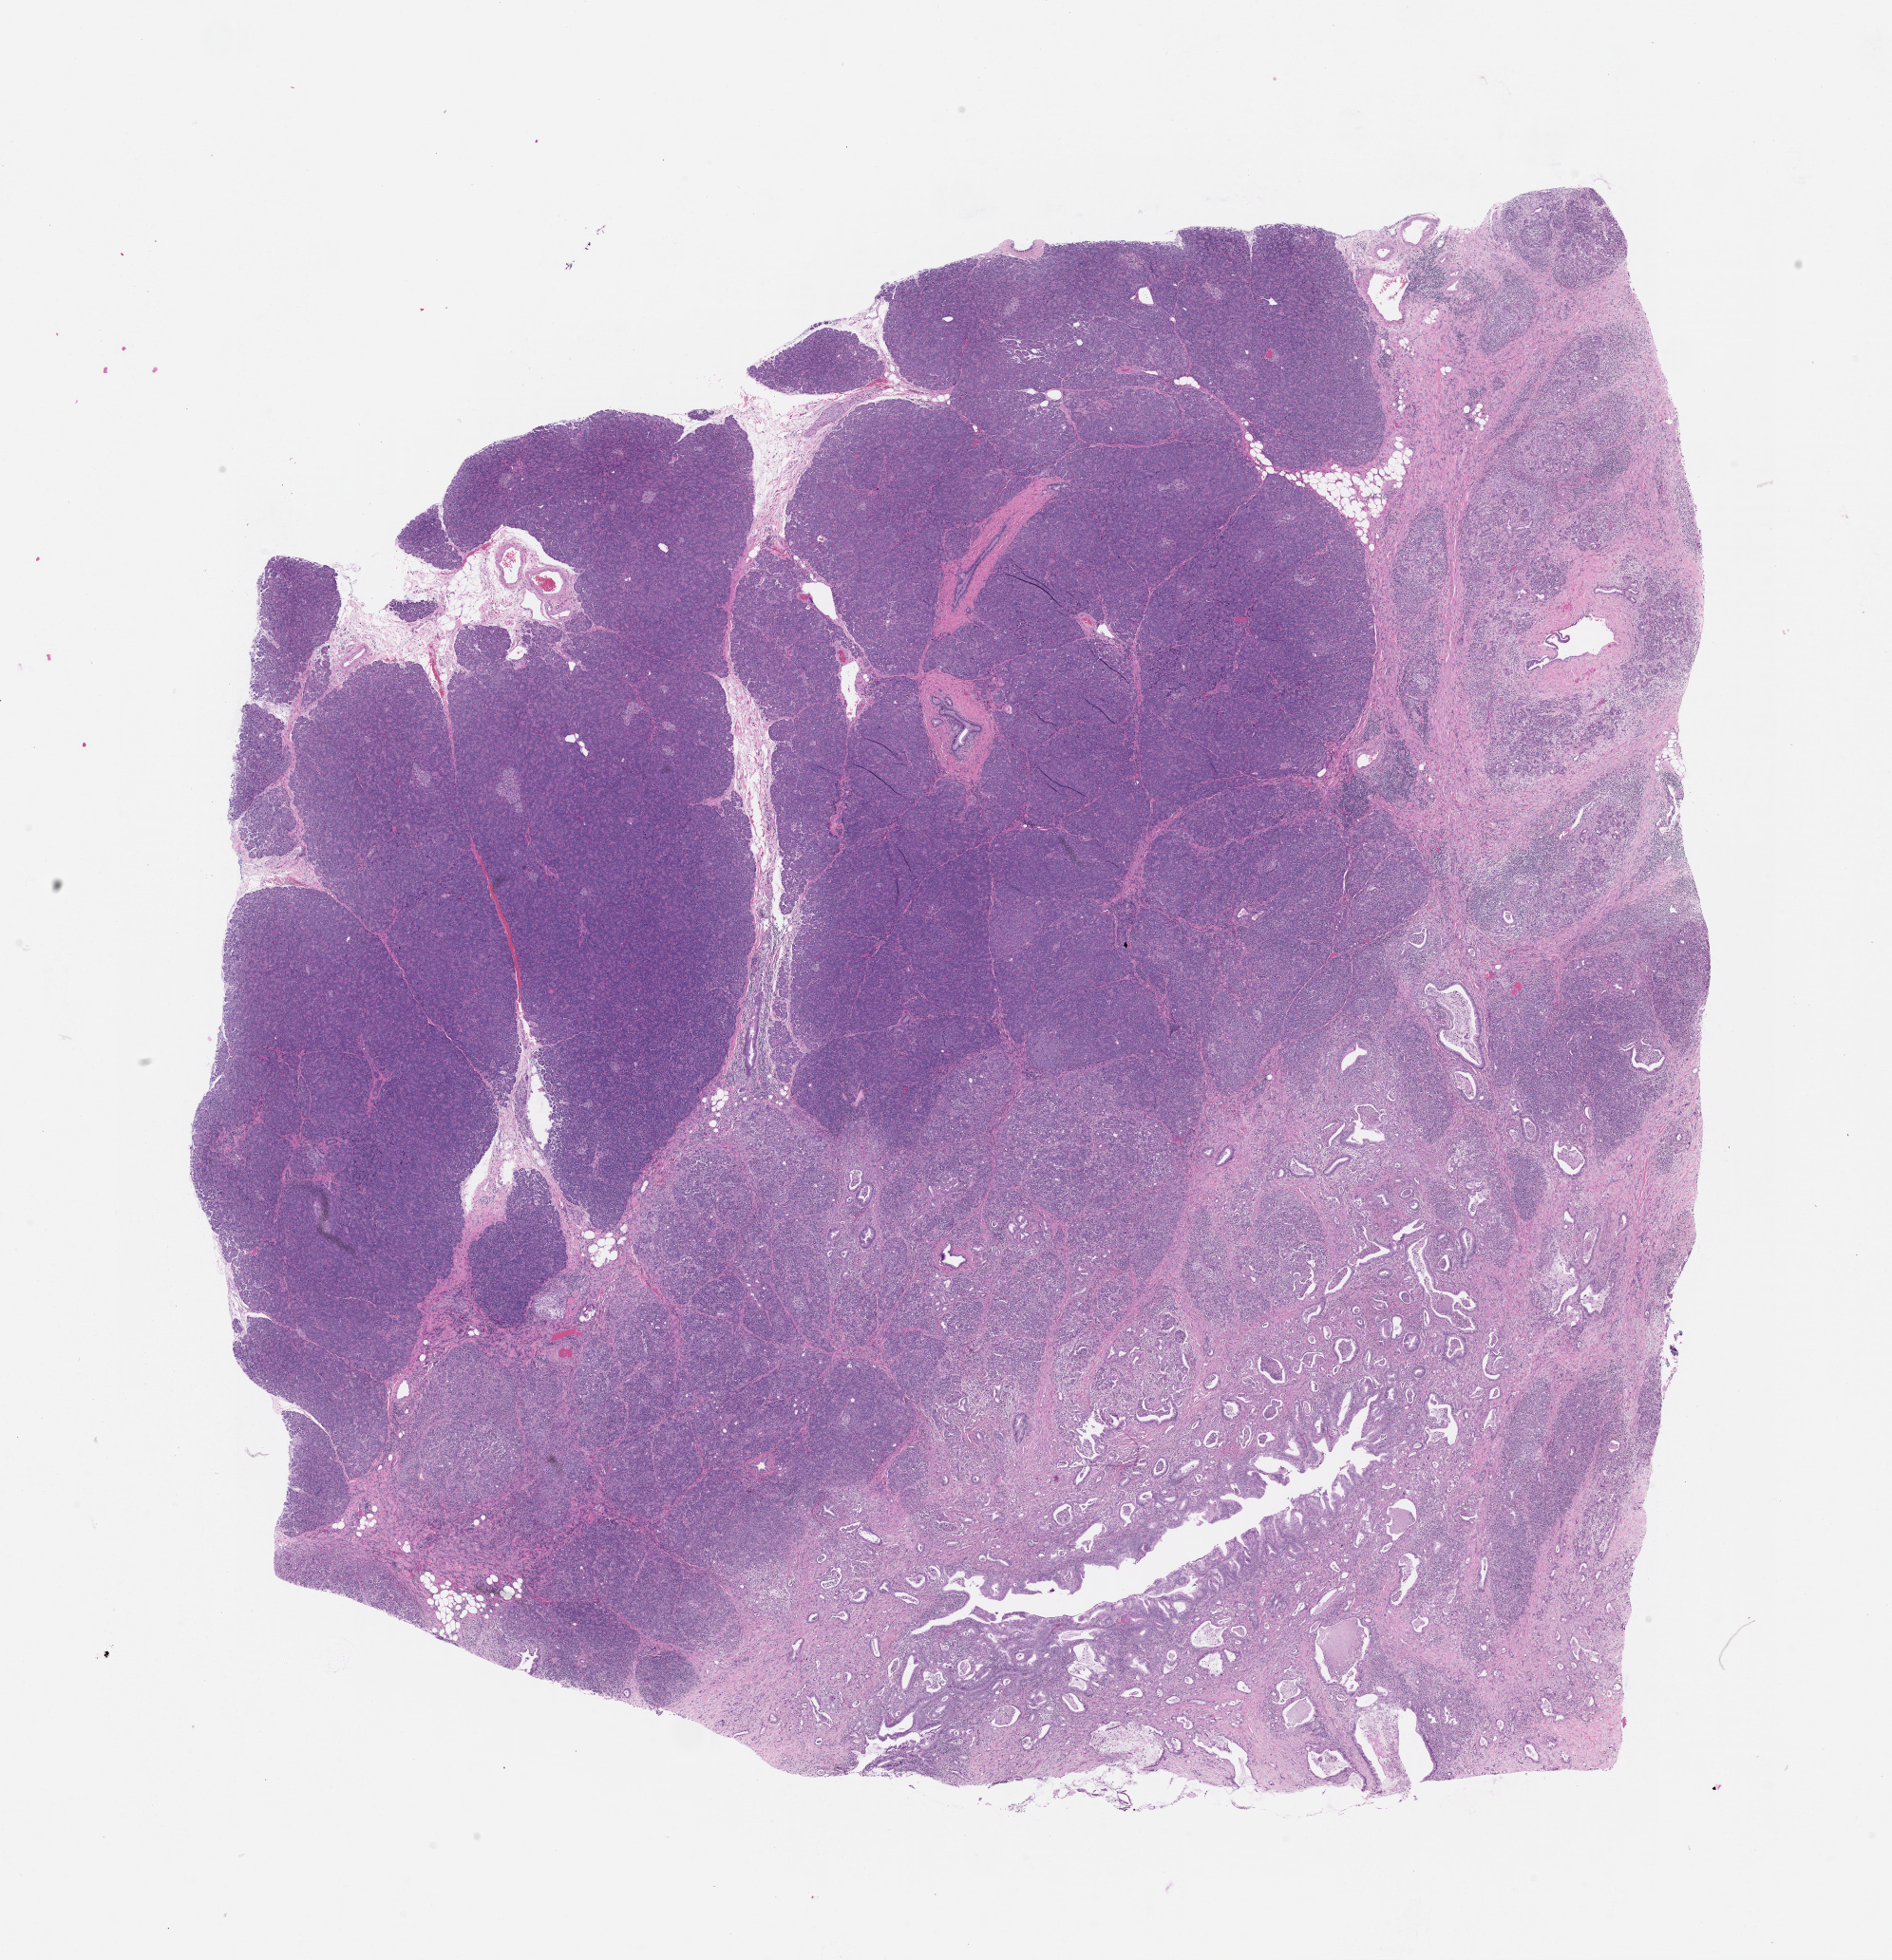
Digitized Hematoxylin and eosin (H&E) stained tissue section (whole slide) — a low-resolution overview of the entire scanned area, about 16.0 x 16.6 mm (slide scanned at 20x); pancreas, tumour tissue. 53-year-old male patient.
• primary tumour site (as recorded): head
• patient diagnosis (cohort enrolment): ductal adenocarcinoma (pancreas)